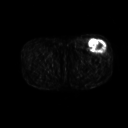
FDG PET of an extremity soft-tissue mass (from a PET/CT study), one axial slice. 3.27 mm slice thickness. 128 × 128 image matrix, field of view 500 × 500 mm. Male patient, age 64 years. Case-level facts recorded for this patient, not image findings: histological type: extraskeletal osteosarcoma; grade: high; site of the primary tumour: thigh.
Outlined on this slice (expert contour drawn on MRI and transferred to this co-registered scan by the dataset authors):
- gross tumour volume (mass): bounding box <89,40,107,53> (left, top, right, bottom; pixels)